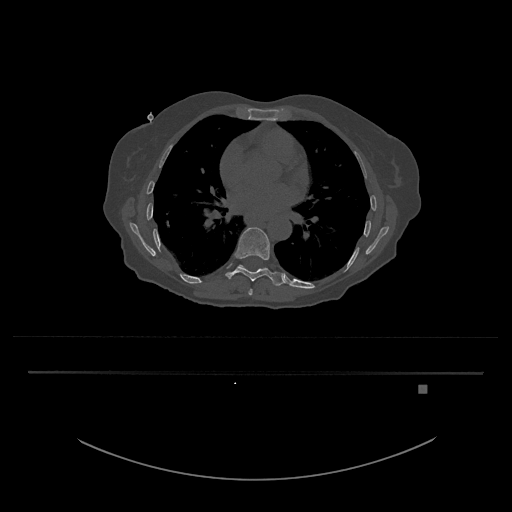
CT including the spine, one axial slice. Position 757 of 797 along the scan axis. Reconstruction kernel Br40s/3. Bone window (W 1800 / L 400 HU). 512 × 512 image matrix, field of view 500 × 500 mm. Patient: female, 57 years. From the clinical record (not read from this slice): primary cancer: cervical.
Annotated regions visible in this slice (semi-automatic segmentation, software-assisted and operator-edited):
- T10 vertebra: bounding box [x1, y1, x2, y2] px = [239, 265, 267, 272]
- T8 vertebra: [248, 289, 253, 296]
- T9 vertebra: [225, 227, 284, 286]